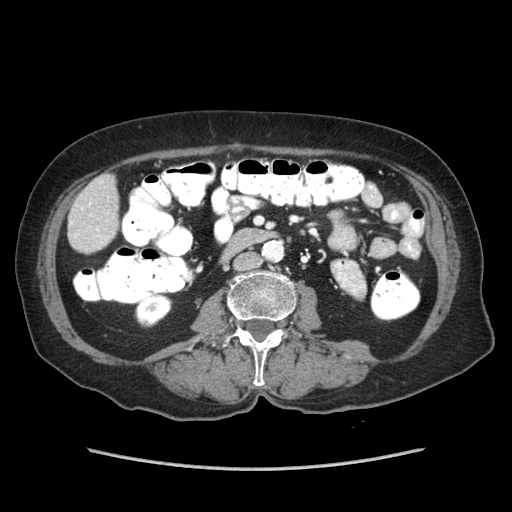
Contrast-enhanced abdominal CT (liver protocol), one axial slice; position 10 of 89 along the scan axis; reconstruction kernel STANDARD; 140 kVp; soft-tissue window (W 400 / L 40 HU); 2.5 mm slice thickness; 512 × 512 image matrix, field of view 360 × 360 mm. From the clinical record (not read from this slice): diagnosis: hepatocellular carcinoma (patient treated with transarterial chemoembolisation; whether this scan precedes or follows treatment is not stated here); TNM stage (as recorded): Stage-IIIA; Child-Pugh class: A; tumour nodularity: multinodular.
Outlined on this slice (semi-automatic segmentation, software-assisted and operator-edited):
- liver parenchyma outside the tumour (the mass and vessels are separate outlines, so this box may not span the whole liver): bounding box <72,174,118,252> (left, top, right, bottom; pixels)